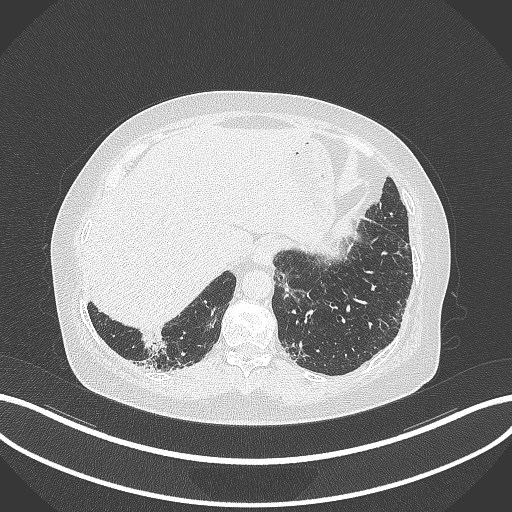
Chest CT, one axial slice; position 16 of 296 along the scan axis; 120 kVp; lung window (W 1500 / L -600 HU); 1 mm slice thickness; 512 × 512 image matrix. Female patient, age 65 years. Case-level facts recorded for this patient, not image findings: clinical TNM (as recorded): T2b N1 M0; histopathological grade: G1.
Outlined on this slice (bounding box drawn by a radiologist):
- lung tumour (recorded histology: adenocarcinoma): box from (x=136, y=331) to (x=172, y=359) px